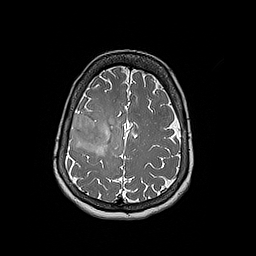
Brain MRI from a brain-tumour surgery series, one axial slice; position 62 of 192 along the scan axis; 1 mm slice thickness; 256 × 256 image matrix. From the clinical record (not read from this slice): histopathology: Oligodendroglioma; WHO grade: 3; IDH mutation: yes; tumour location: Right Frontal.
Annotated regions visible in this slice (manually delineated by an expert):
- tumour: bounding box <69,114,108,151> (left, top, right, bottom; pixels)